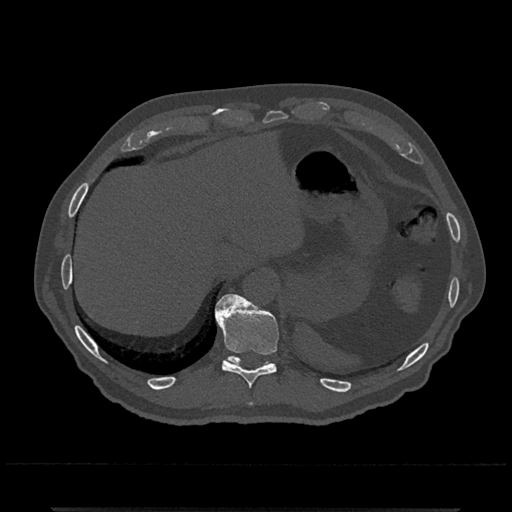
CT including the spine, one axial slice. Position 542 of 797 along the scan axis. Reconstruction kernel Br40s/3. Bone window (W 1800 / L 400 HU). 512 × 512 image matrix, field of view 393 × 393 mm. Patient: male, 67 years. From the clinical record (not read from this slice): primary cancer: prostate.
Outlined on this slice (semi-automatically segmented with operator editing):
- T10 vertebra: bounding box <214,293,279,389> (left, top, right, bottom; pixels)
- T11 vertebra: <225,356,271,367>